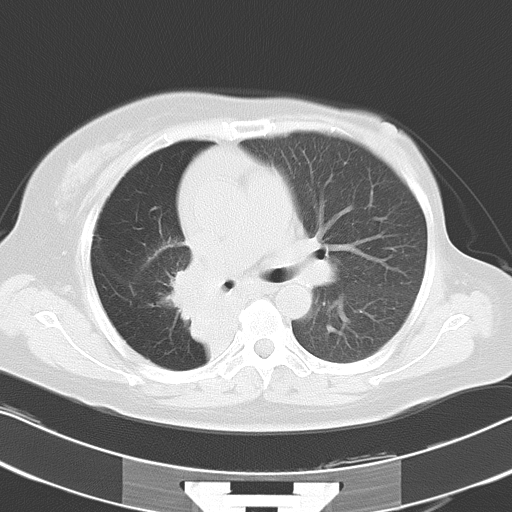
Chest CT, one axial slice. Position 19 of 30 along the scan axis. Reconstruction kernel B70f. 120 kVp. Lung window (W 1500 / L -600 HU). 512 × 512 image matrix, field of view 331 × 331 mm. Patient: female, 53 years. Case-level facts recorded for this patient, not image findings: clinical TNM (as recorded): T2b N1 M0.
Outlined on this slice (rectangle marked by the reading radiologist):
- lung tumour (recorded histology: adenocarcinoma): bounding box (x1, y1, x2, y2) in pixels: (164, 259, 227, 342)